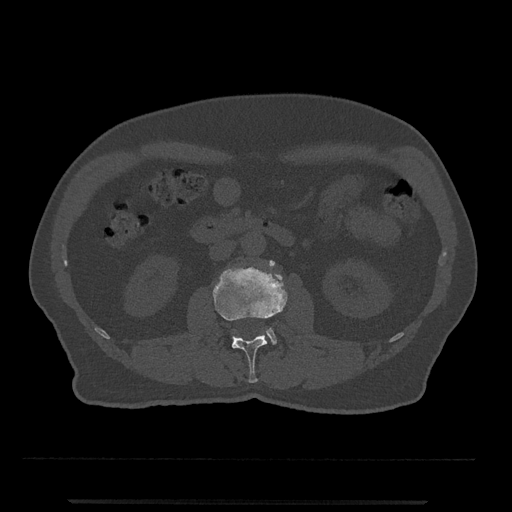
CT including the spine, one axial slice. 120 kVp. Bone window (W 1800 / L 400 HU). 0.5 mm slice thickness. 512 × 512 image matrix. Patient: male, 63 years. Case-level facts recorded for this patient, not image findings: primary cancer: prostate.
Structures marked on this image (semi-automatically segmented with operator editing):
- L2 vertebra: box from (x=213, y=260) to (x=288, y=383) px
- L3 vertebra: (x=266, y=261)–(x=277, y=344)